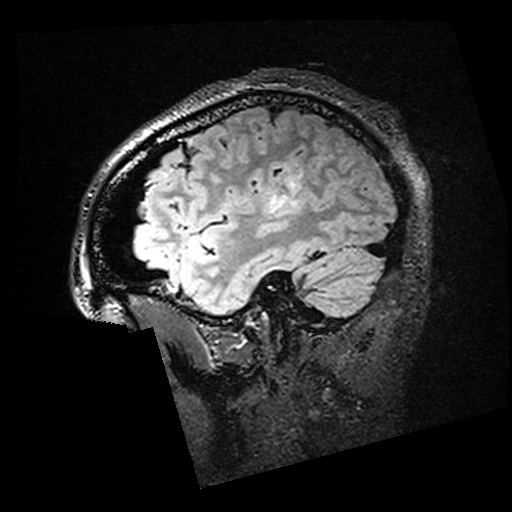
Brain MRI from a brain-tumour surgery series, one sagittal slice. T2 FLAIR. 1 mm slice thickness. 512 × 512 image matrix, field of view 250 × 250 mm. Case-level facts recorded for this patient, not image findings: histopathology: Oligodendroglioma; WHO grade: 2; IDH mutation: yes; tumour location: Left Posterior Temporal.
Annotated regions visible in this slice (outlined manually by an expert reader):
- residual tumour: bounding box <289,175,302,188> (left, top, right, bottom; pixels)